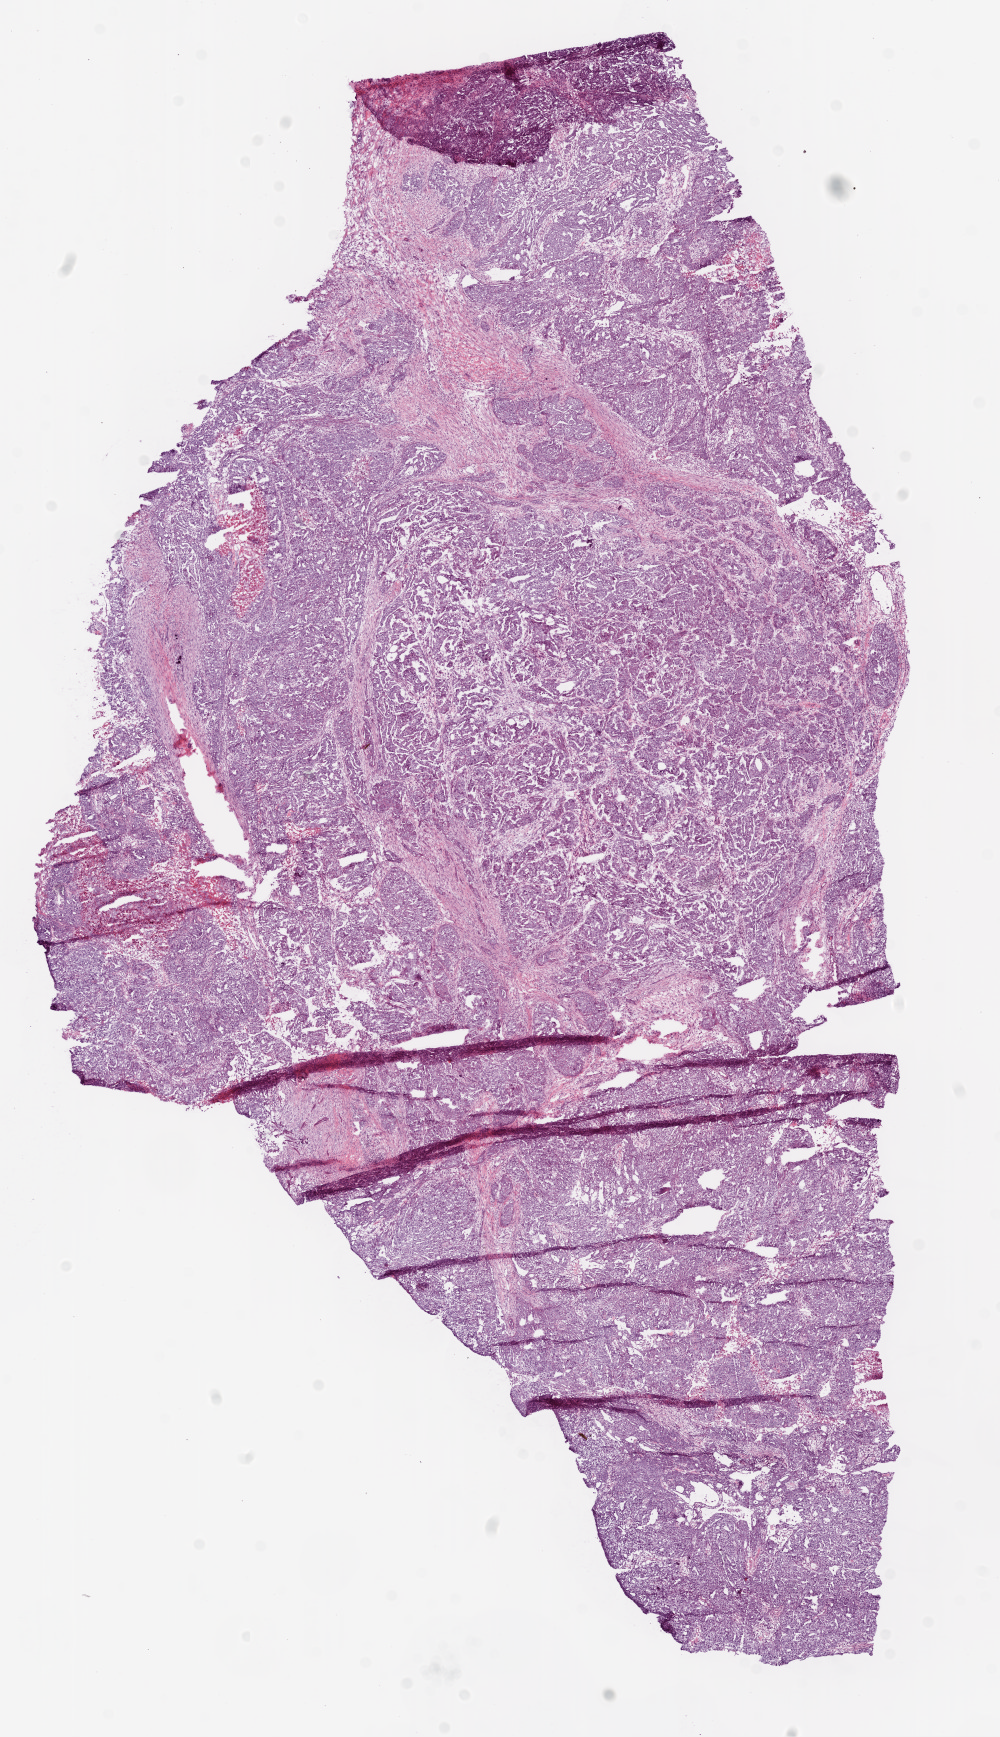
Whole-slide histology image, H&E — low-resolution overview of the scanned area, about 8.0 x 13.9 mm, frozen section from the top of the tissue portion, ovary, primary tumour sample. Patient: female, age at initial diagnosis 80 years. Histologic grade: G3 (poorly differentiated). Slide review estimates, as recorded: tumour cells 90%, tumour nuclei 95%, normal cells 0%, stromal cells 5%, necrosis 5%.
• diagnosis: Serous cystadenocarcinoma, NOS
• FIGO stage: IIIC